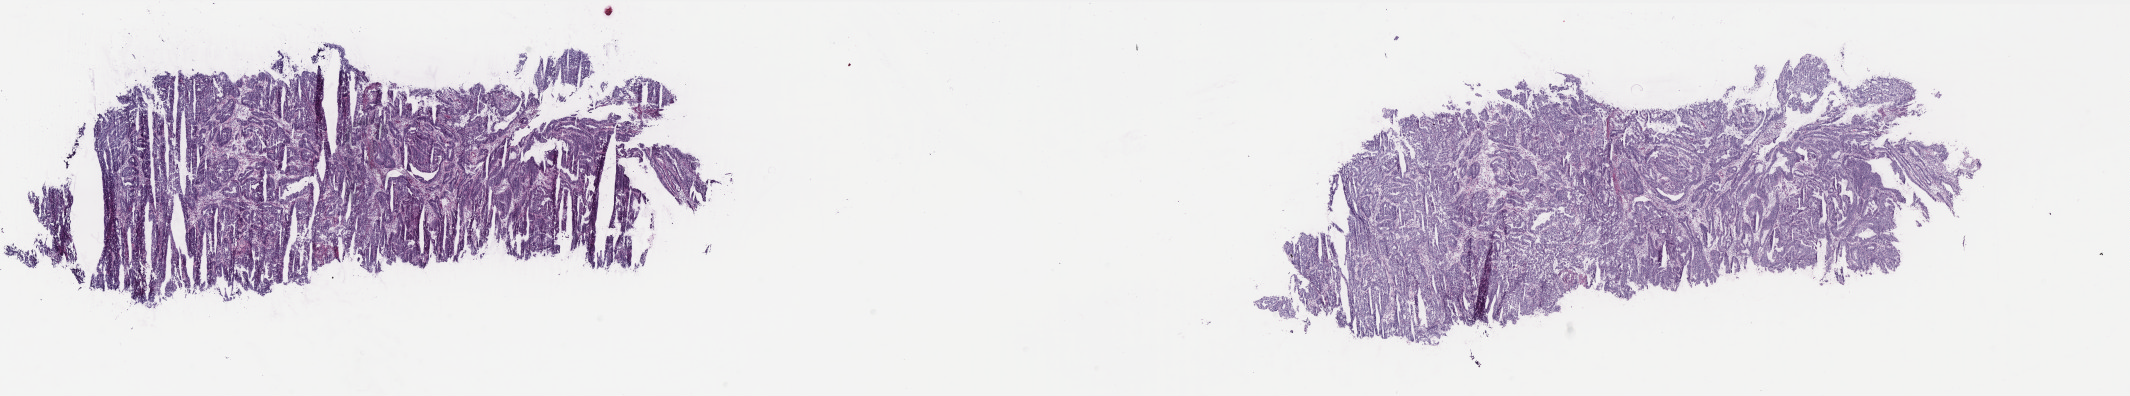
Digitized H&E tissue section (whole slide) — low-resolution overview of the scanned area, about 34.2 x 6.3 mm (acquisition: 40x scan); frozen section from the top of the tissue portion; primary tumour sample from the uterus. Patient: female, age at initial diagnosis 60 years. Histologic grade: G3 (poorly differentiated). Composition of this section per pathologist review: tumour cells 100%, tumour nuclei 75%, normal cells 0%, stromal cells 0%, necrosis 0%. Infiltration values recorded for this section: lymphocyte infiltration 0%, monocyte infiltration 0%, neutrophil infiltration 0%.
Diagnosis: Endometrioid adenocarcinoma, NOS (endometrium). FIGO stage: IA.